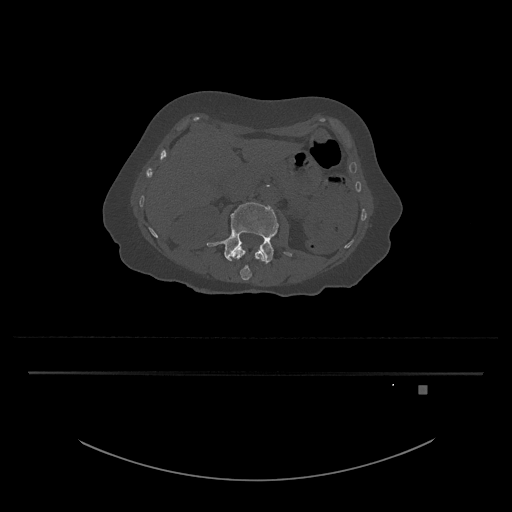
CT including the spine, one axial slice. Slice 451 of 797 in the series (ordered by position). Reconstruction kernel Br40s/3. 120 kVp. Bone window (W 1800 / L 400 HU). 512 × 512 image matrix, field of view 500 × 500 mm. Patient: female, 57 years. Case-level facts recorded for this patient, not image findings: primary cancer: cervical.
Outlined on this slice (semi-automatically segmented with operator editing):
- L3 vertebra: bounding box [x1, y1, x2, y2] px = [207, 202, 292, 264]